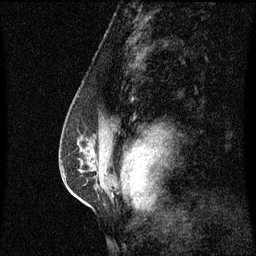
Breast MRI (dynamic contrast-enhanced), one sagittal slice; slice 37 of 60 in the series (ordered by position); dynamic contrast-enhanced series, image 2 of 3 at this slice position (ordered by acquisition); 1.5 T; TE 4.2 ms, TR 8.9 ms; 256 × 256 image matrix, field of view 200 × 200 mm. Female patient, age 50 years. Case-level facts recorded for this patient, not image findings: setting: breast cancer imaged before/during neoadjuvant chemotherapy; receptor status: triple-negative.
Outlined on this slice (semi-automatic segmentation, software-assisted and operator-edited):
- analysis volume of interest (the breast-tissue region the enhancement analysis was run in; not a lesion): bounding box (x1, y1, x2, y2) in pixels: (61, 90, 101, 205)
- tumour enhancement mask (voxels above the 70 % enhancement threshold inside the analysis volume of interest): (92, 154, 96, 159)